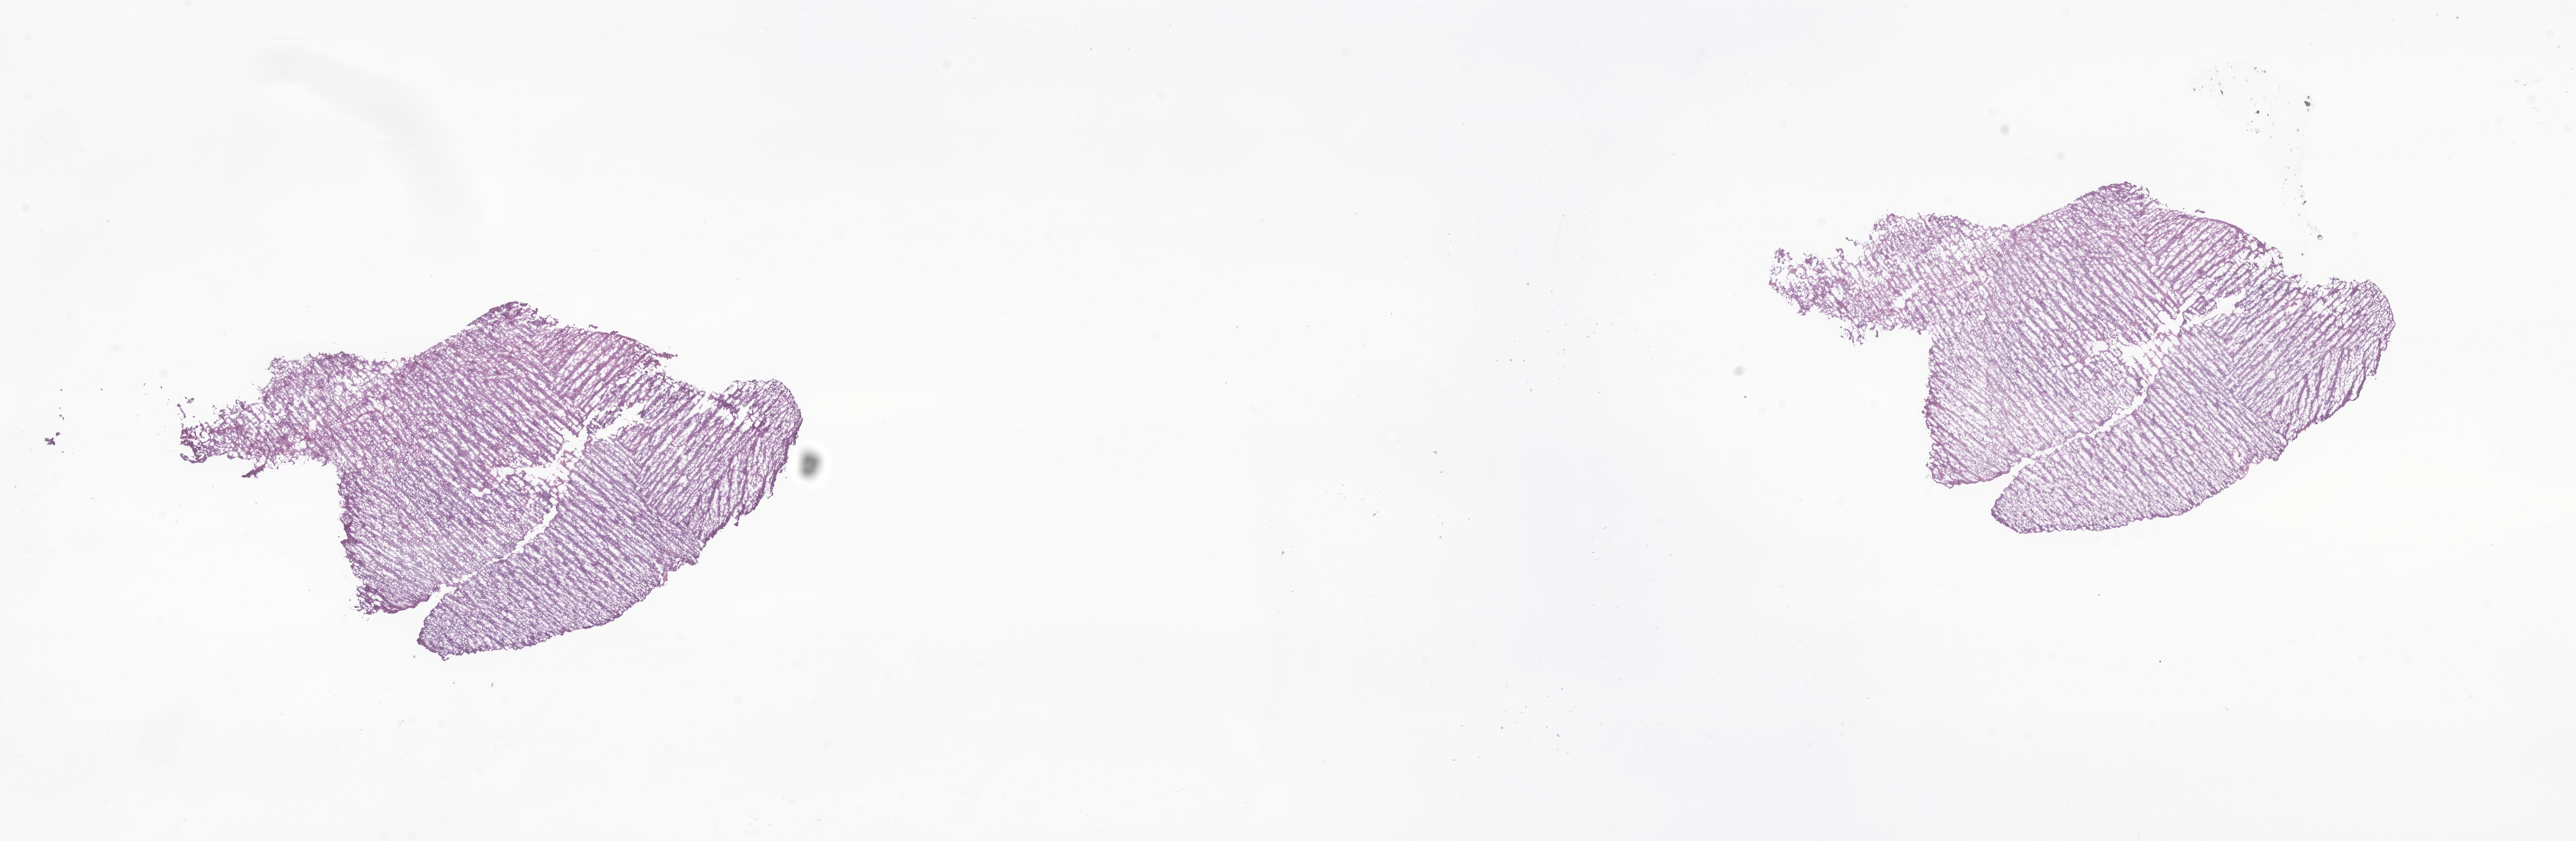
Haematoxylin and eosin whole-slide image of tumor tissue from the frontal lobe, whole scanned area (about 27.5 x 9.0 mm) shown as a low-resolution overview; frozen section. Patient female; age 311 days.
Recorded diagnosis: Neoplasm, malignant.